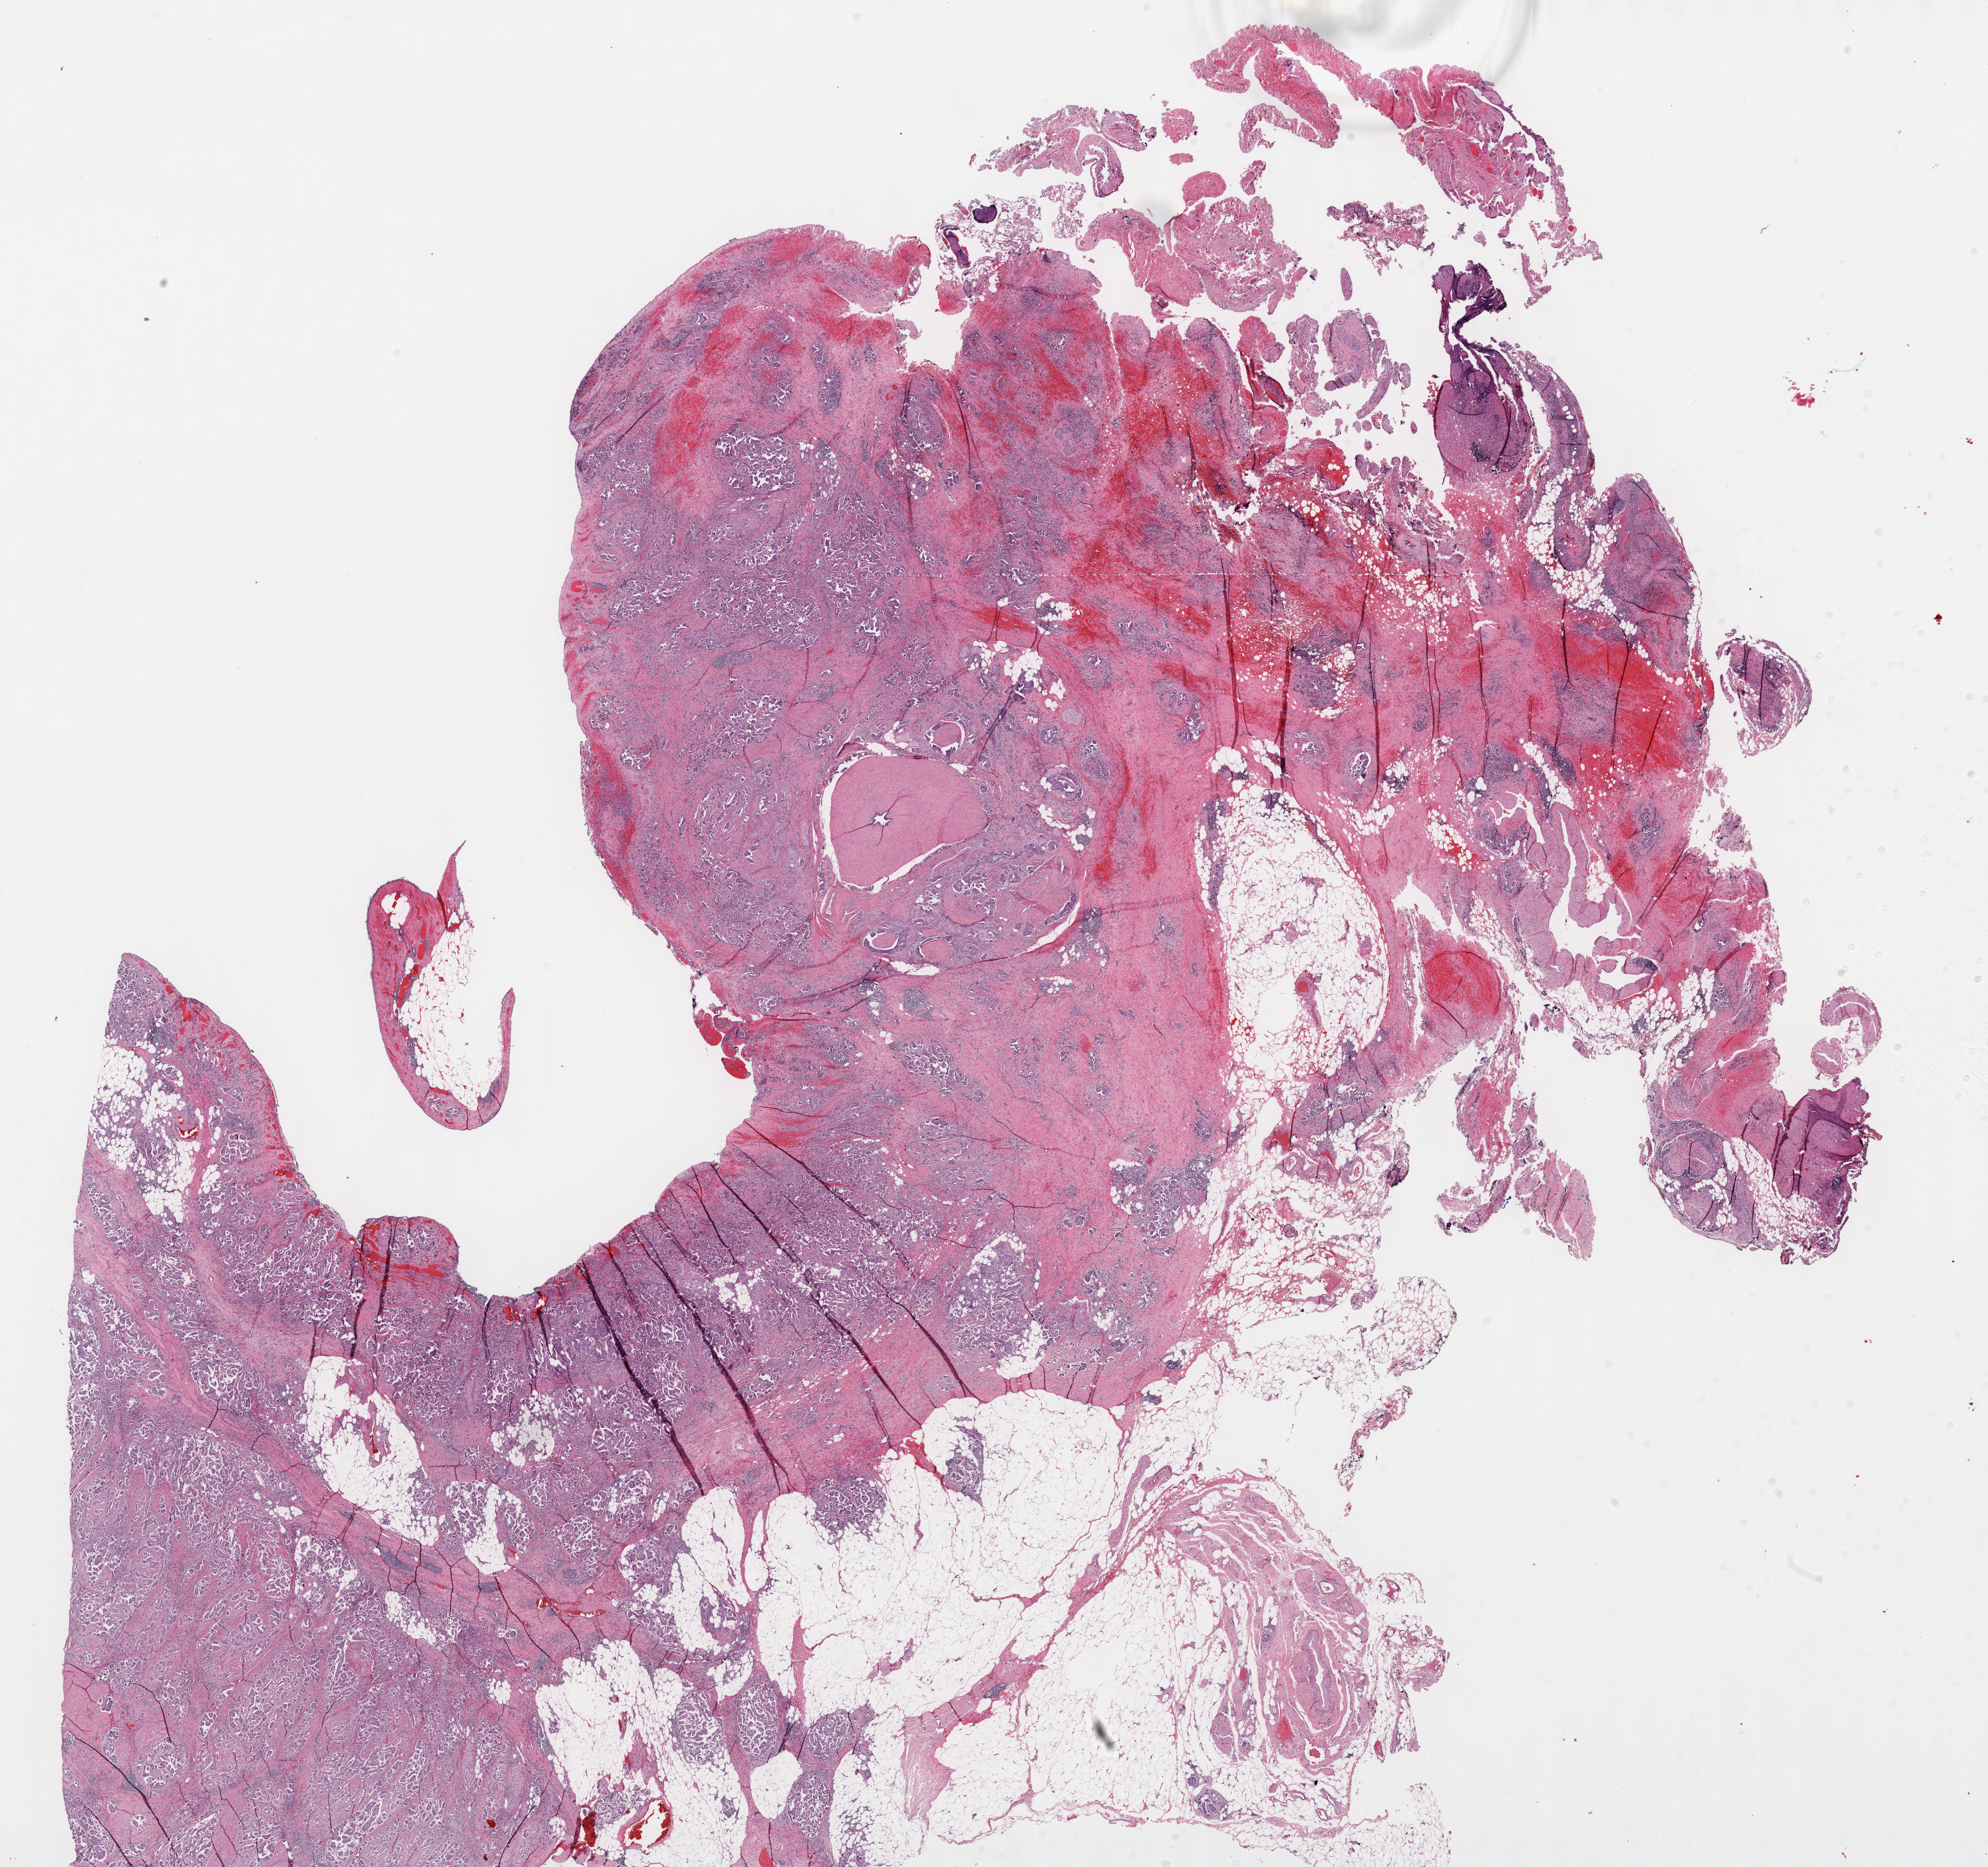
Hematoxylin and eosin (H&E) stained whole-slide image, shown as a low-resolution overview of the whole scanned area (about 24.1 x 22.7 mm), FFPE section, primary tumour sample from the bladder. Male, age 75 years at initial diagnosis. Histologic grade: high grade.
AJCC pathologic stage: IV (7th edition). Lymph nodes positive (case pathology): 4 of 4 examined. Histologic diagnosis: Transitional cell carcinoma.